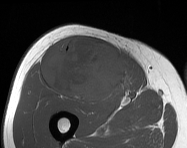
MRI of an extremity soft-tissue mass, one axial slice; MR volume resampled by the dataset authors to the PET/CT grid (not the native acquisition matrix); 3.27 mm slice thickness; 187 × 148 image matrix. Male patient. Case-level facts recorded for this patient, not image findings: histological type: pleiomorphic leiomyosarcoma; grade: intermediate; site of the primary tumour: right thigh.
Annotated regions visible in this slice (expert contour drawn on MRI and transferred to this co-registered scan by the dataset authors):
- gross tumour volume including surrounding oedema: bounding box <43,36,131,103> (left, top, right, bottom; pixels)
- gross tumour volume (mass): <43,36,131,103>